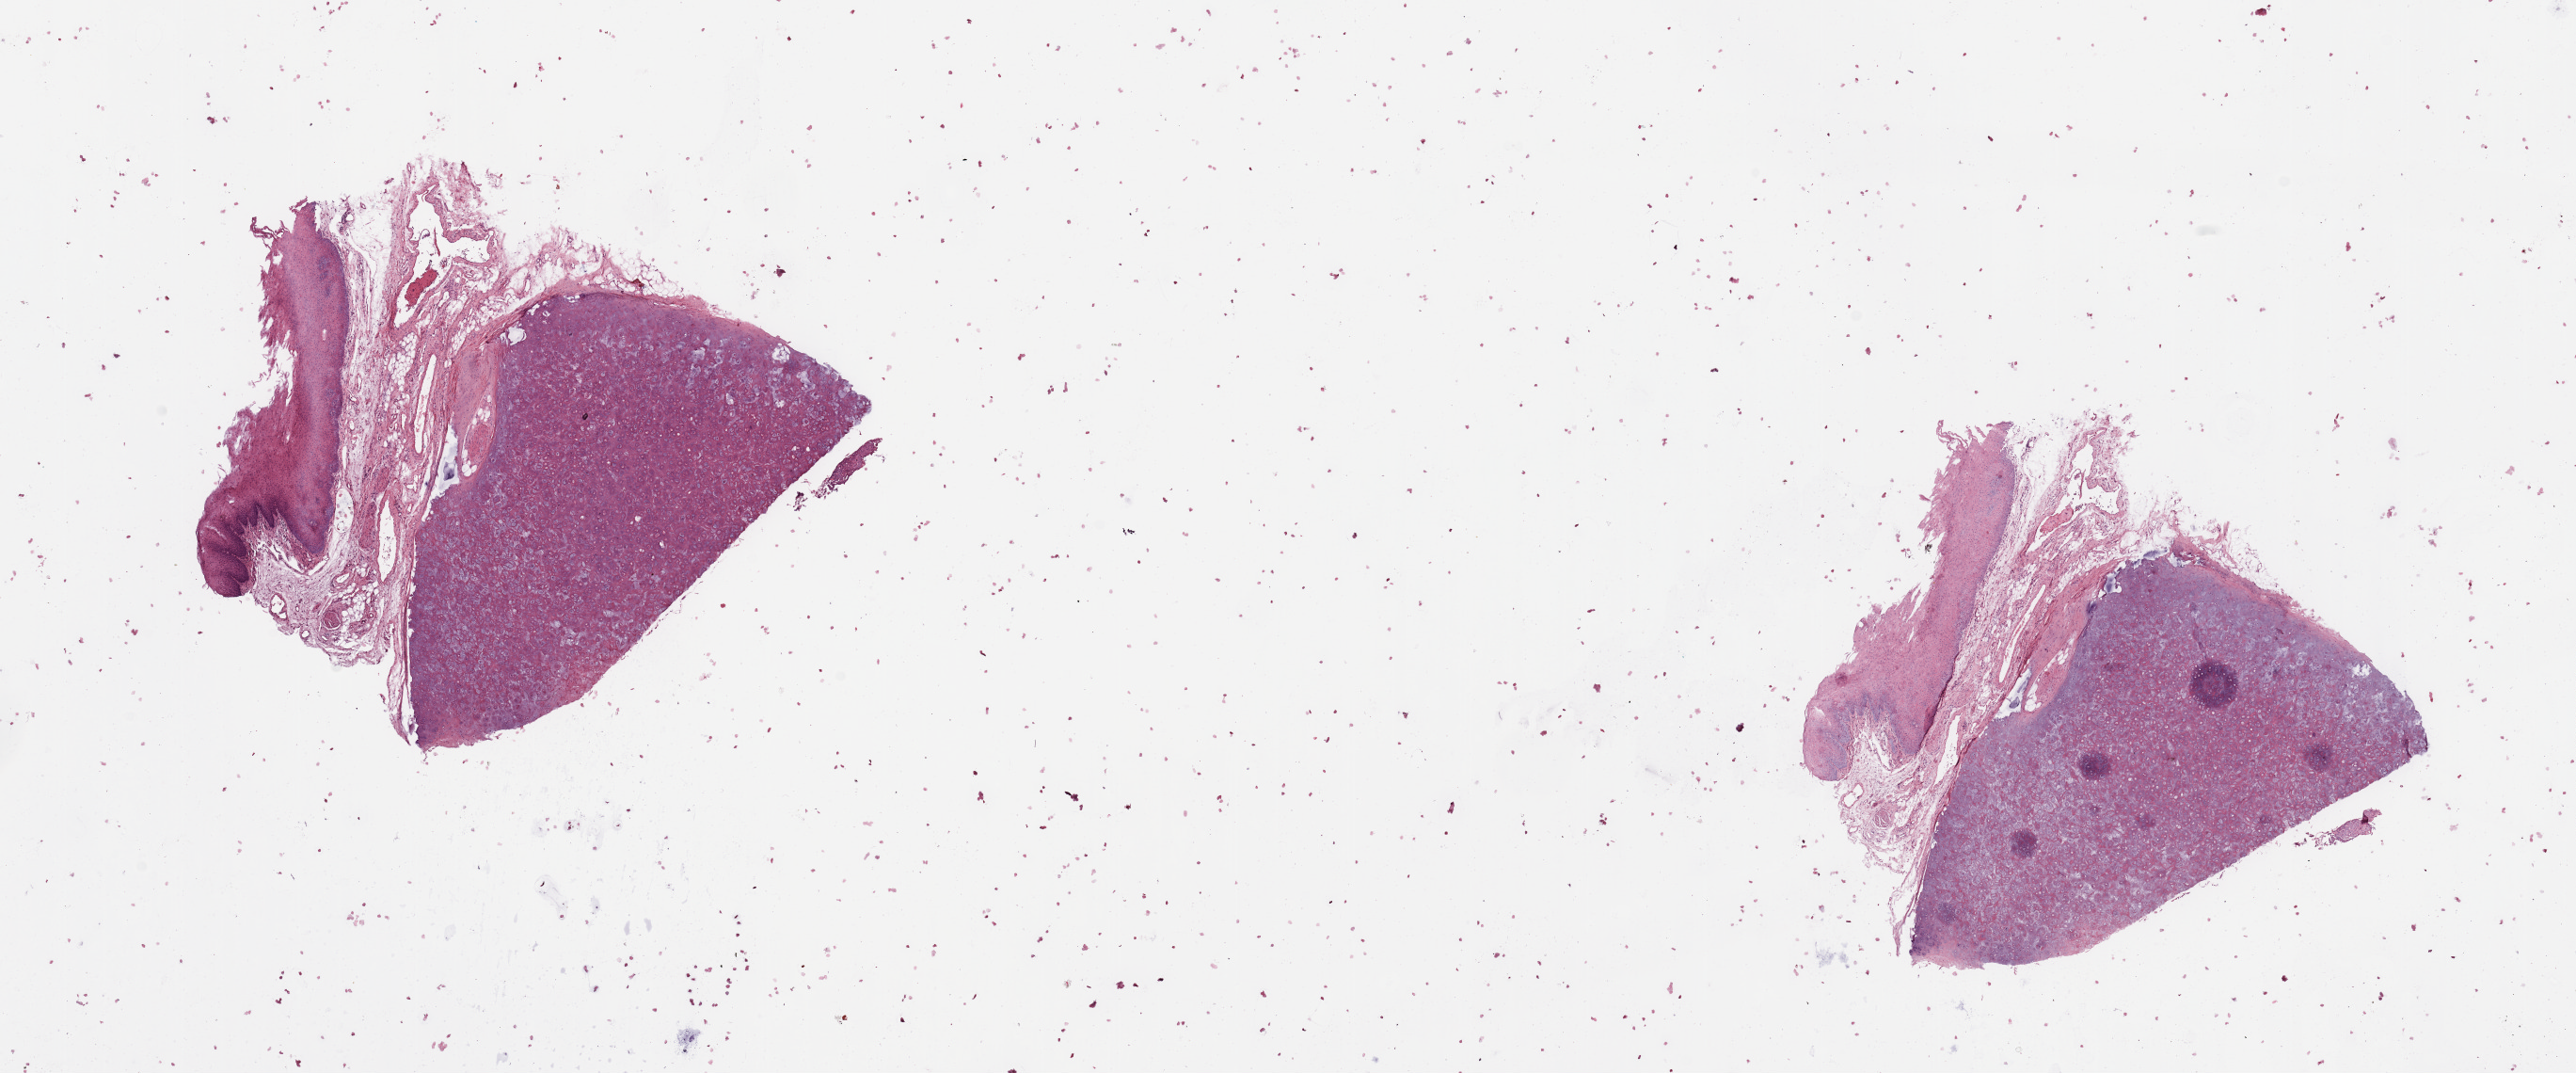
Whole-slide histology image, Hematoxylin and eosin (H&E) stained, whole scanned area (about 21.7 x 9.0 mm, acquisition: 20x scan) shown as a low-resolution overview, normal (non-tumour) tissue sample, sampled site: larynx. Male, 52 y/o.
This section: normal (non-tumour) tissue from the same patient. Patient diagnosis: Squamous cell carcinoma, NOS.